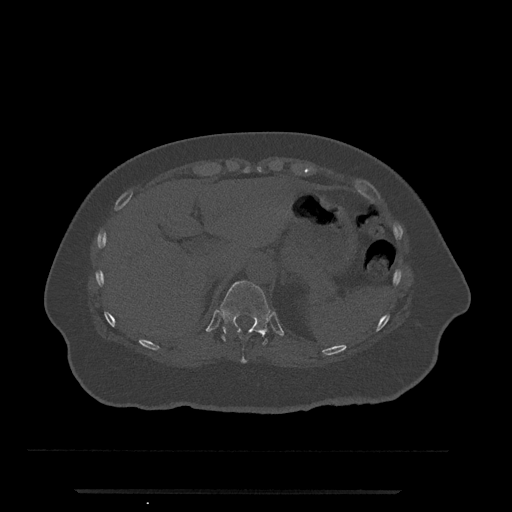
CT including the spine, one axial slice; position 246 of 797 along the scan axis; reconstruction kernel Br40s/3; 120 kVp; bone window (W 1800 / L 400 HU); 0.5 mm slice thickness; 512 × 512 image matrix, field of view 440 × 440 mm. Patient: female, 51 years. Case-level facts recorded for this patient, not image findings: primary cancer: neuro; vertebrae with lytic lesions (as recorded): T8.
Outlined on this slice (semi-automatic segmentation, software-assisted and operator-edited):
- T10 vertebra: bounding box <240,338,247,363> (left, top, right, bottom; pixels)
- T11 vertebra: <220,281,271,345>